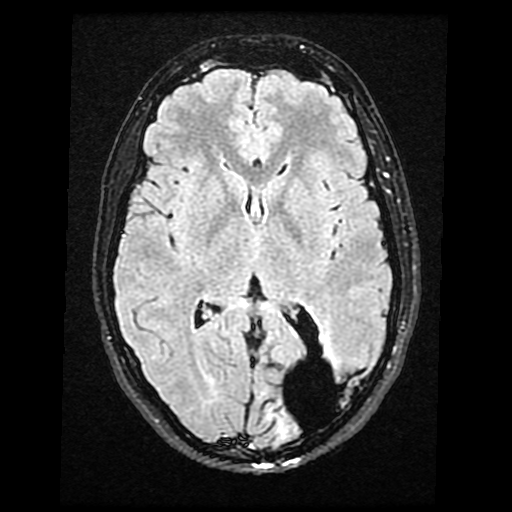
Brain MRI from a brain-tumour surgery series, one axial slice; position 21 of 40 along the scan axis; T2 FLAIR; 512 × 512 image matrix, field of view 240 × 240 mm. From the clinical record (not read from this slice): histopathology: Glioma with ependymal features; WHO grade: 2; tumour location: Left Parietal.
Outlined on this slice (outlined manually by an expert reader):
- tumour: bounding box (x1, y1, x2, y2) in pixels: (265, 359, 338, 436)